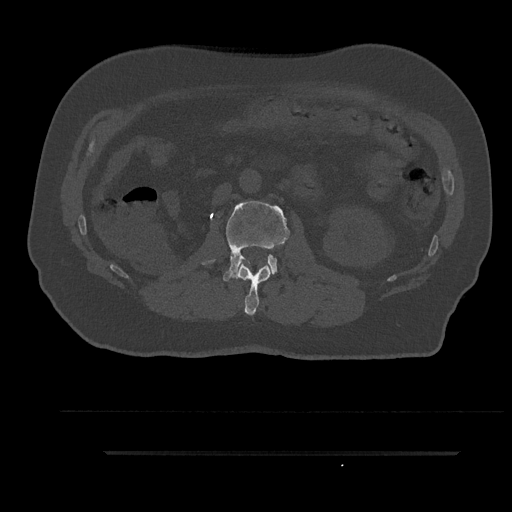
CT including the spine, one axial slice; reconstruction kernel Br40s/3; 120 kVp; bone window (W 1800 / L 400 HU); 512 × 512 image matrix, field of view 432 × 432 mm. Male patient, age 63 years. From the clinical record (not read from this slice): primary cancer: renal; vertebrae with lytic lesions (as recorded): T8.
Annotated regions visible in this slice (semi-automatically segmented with operator editing):
- L1 vertebra: box from (x=232, y=263) to (x=271, y=315) px
- L2 vertebra: (x=203, y=201)–(x=290, y=281)